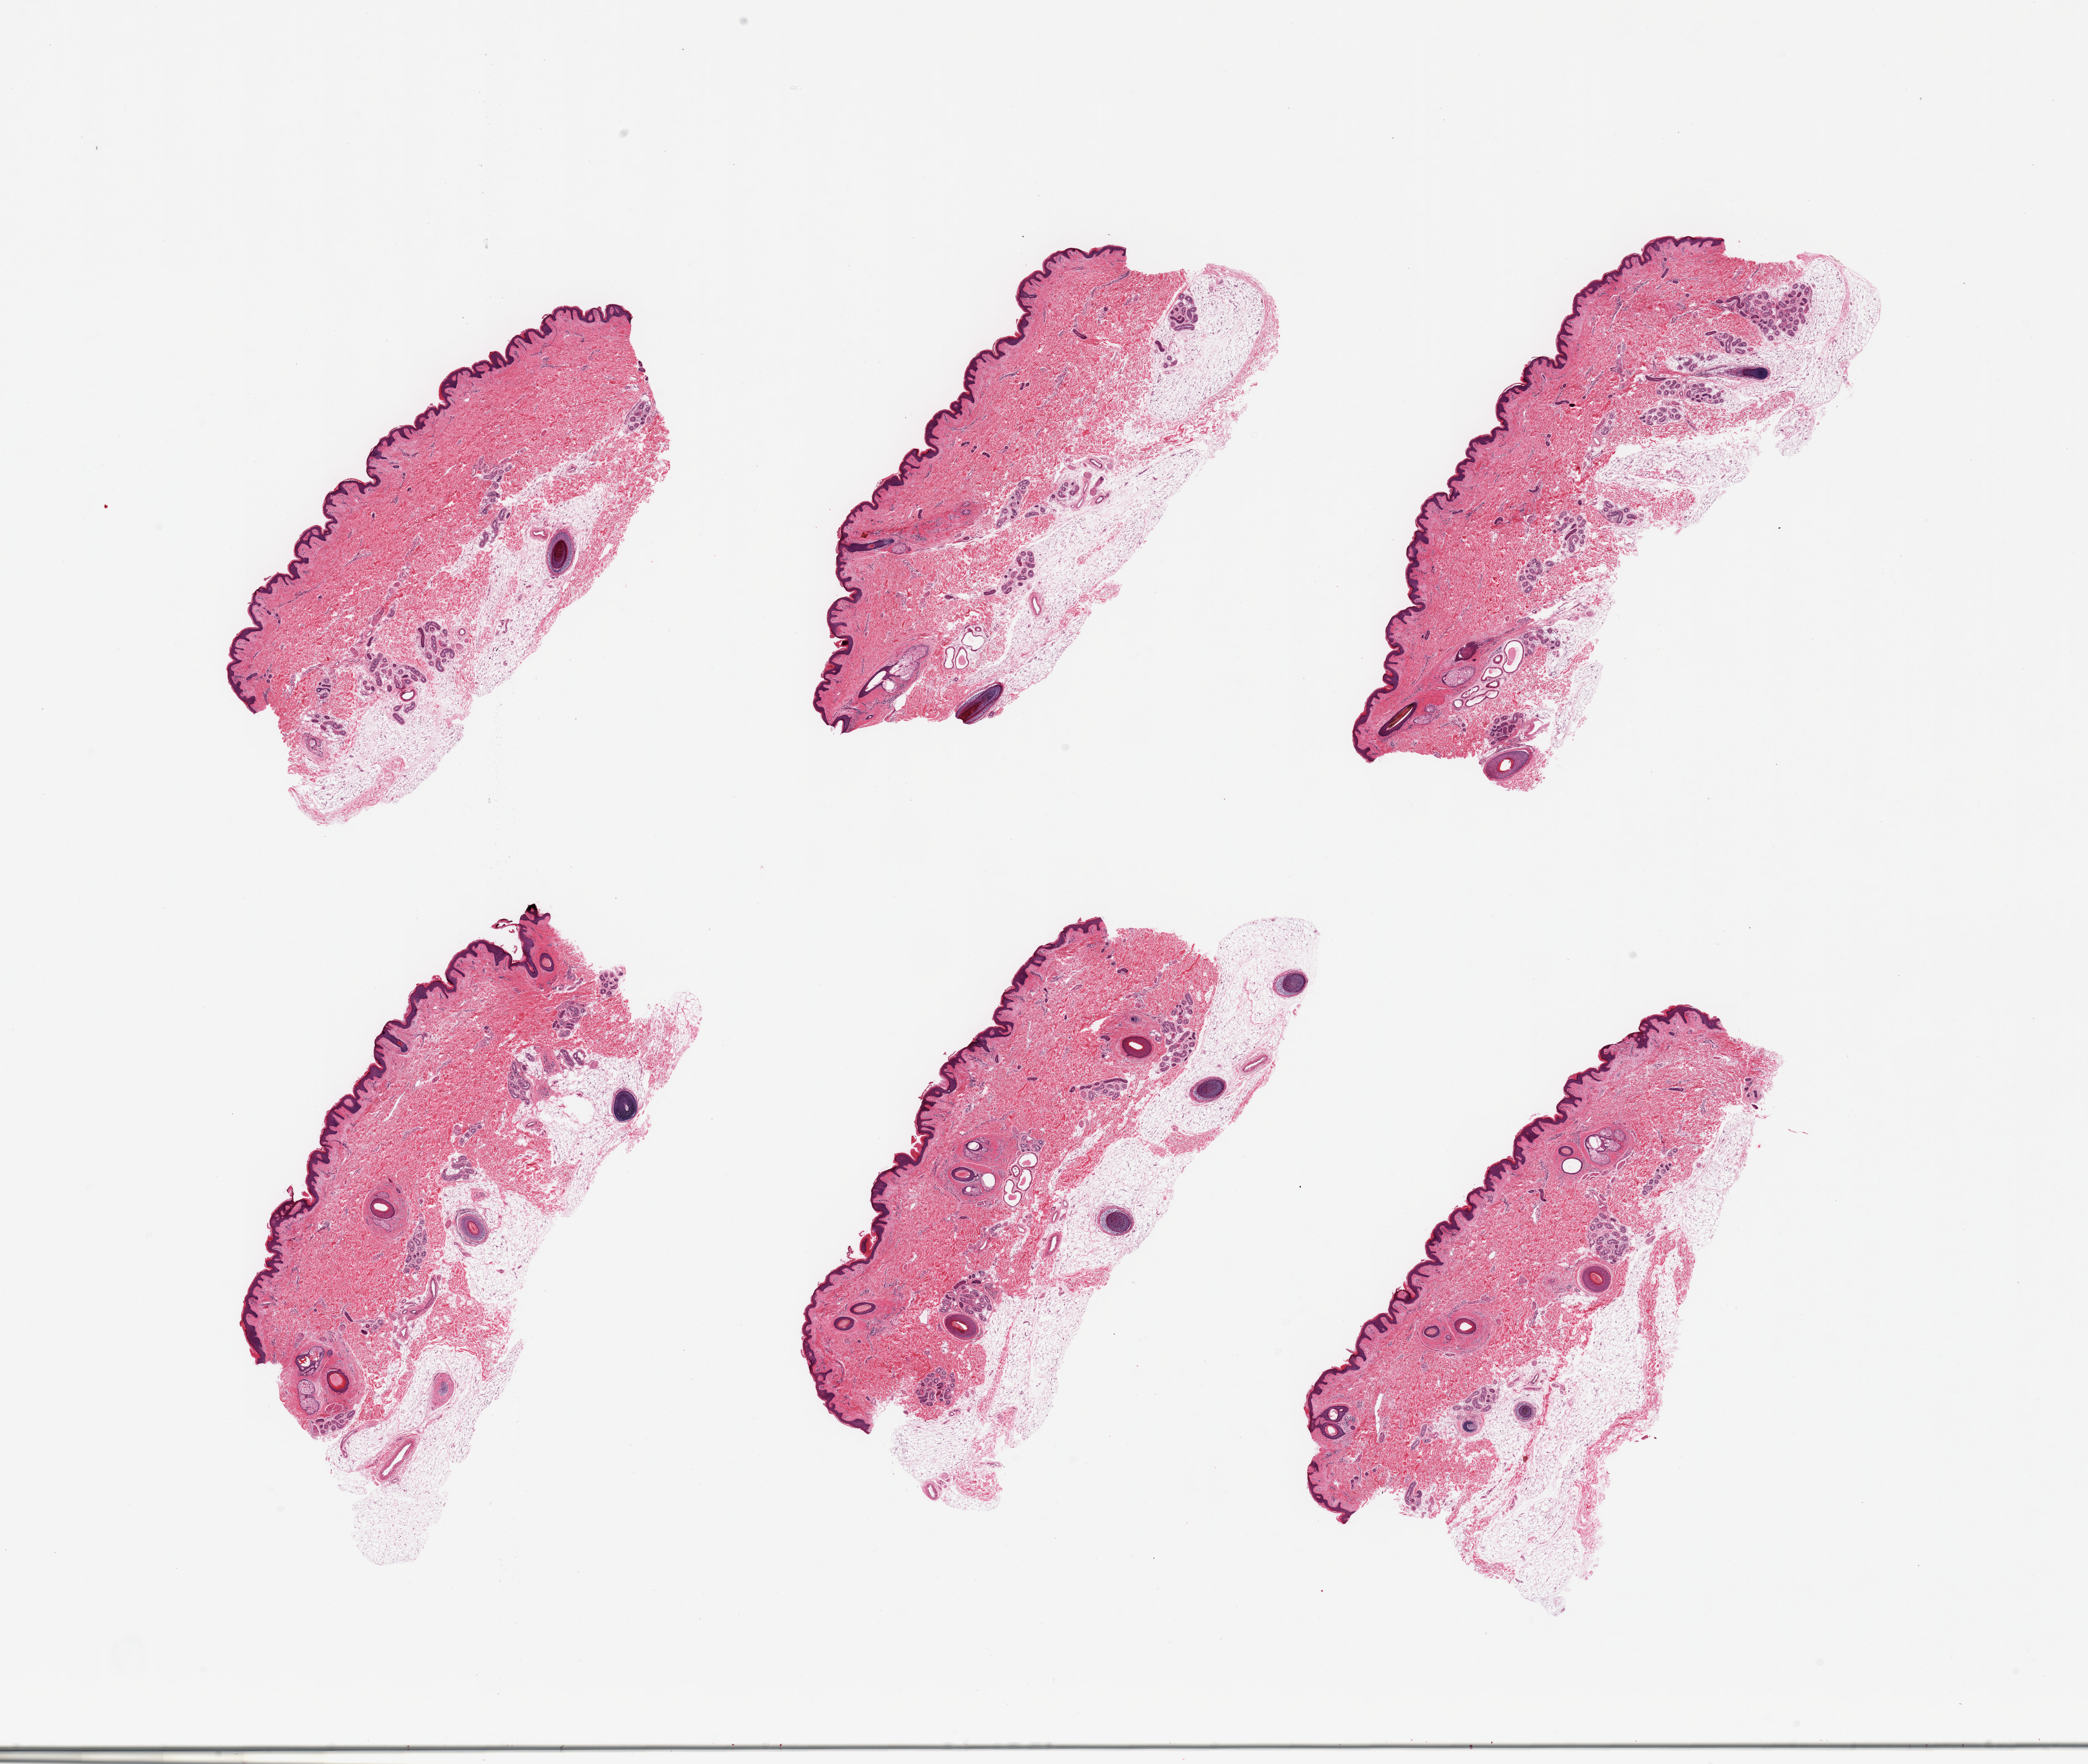
Digitized H&E-stained section, brightfield — shown as a low-resolution overview of the whole scanned area (about 25.6 x 21.6 mm). PAXgene-fixed, paraffin-embedded tissue. Section of skin of suprapubic region (target tissue). Tissue donor sample. Male donor.
Pathologist's review note for this sample: 6 pieces; hair bearing skin with up to 40% external fat.